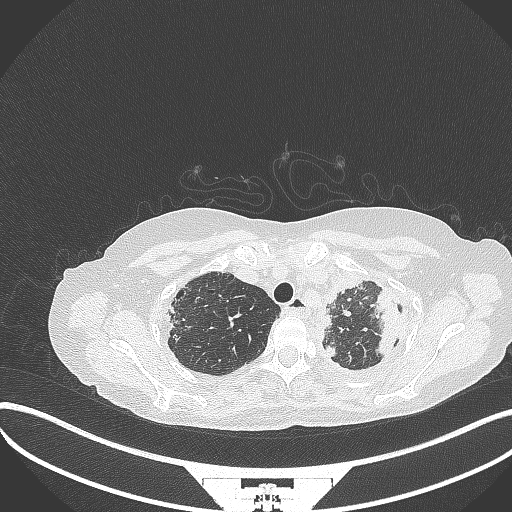
Chest CT, one axial slice; slice 287 of 373 in the series (ordered by position); reconstruction kernel B70f; lung window (W 1500 / L -600 HU); 1 mm slice thickness; 512 × 512 image matrix. Patient: female, 56 years. Case-level facts recorded for this patient, not image findings: clinical TNM (as recorded): T1 N0 M0.
Outlined on this slice (bounding box drawn by a radiologist):
- lung tumour (recorded histology: adenocarcinoma): bounding box <370,289,409,362> (left, top, right, bottom; pixels)